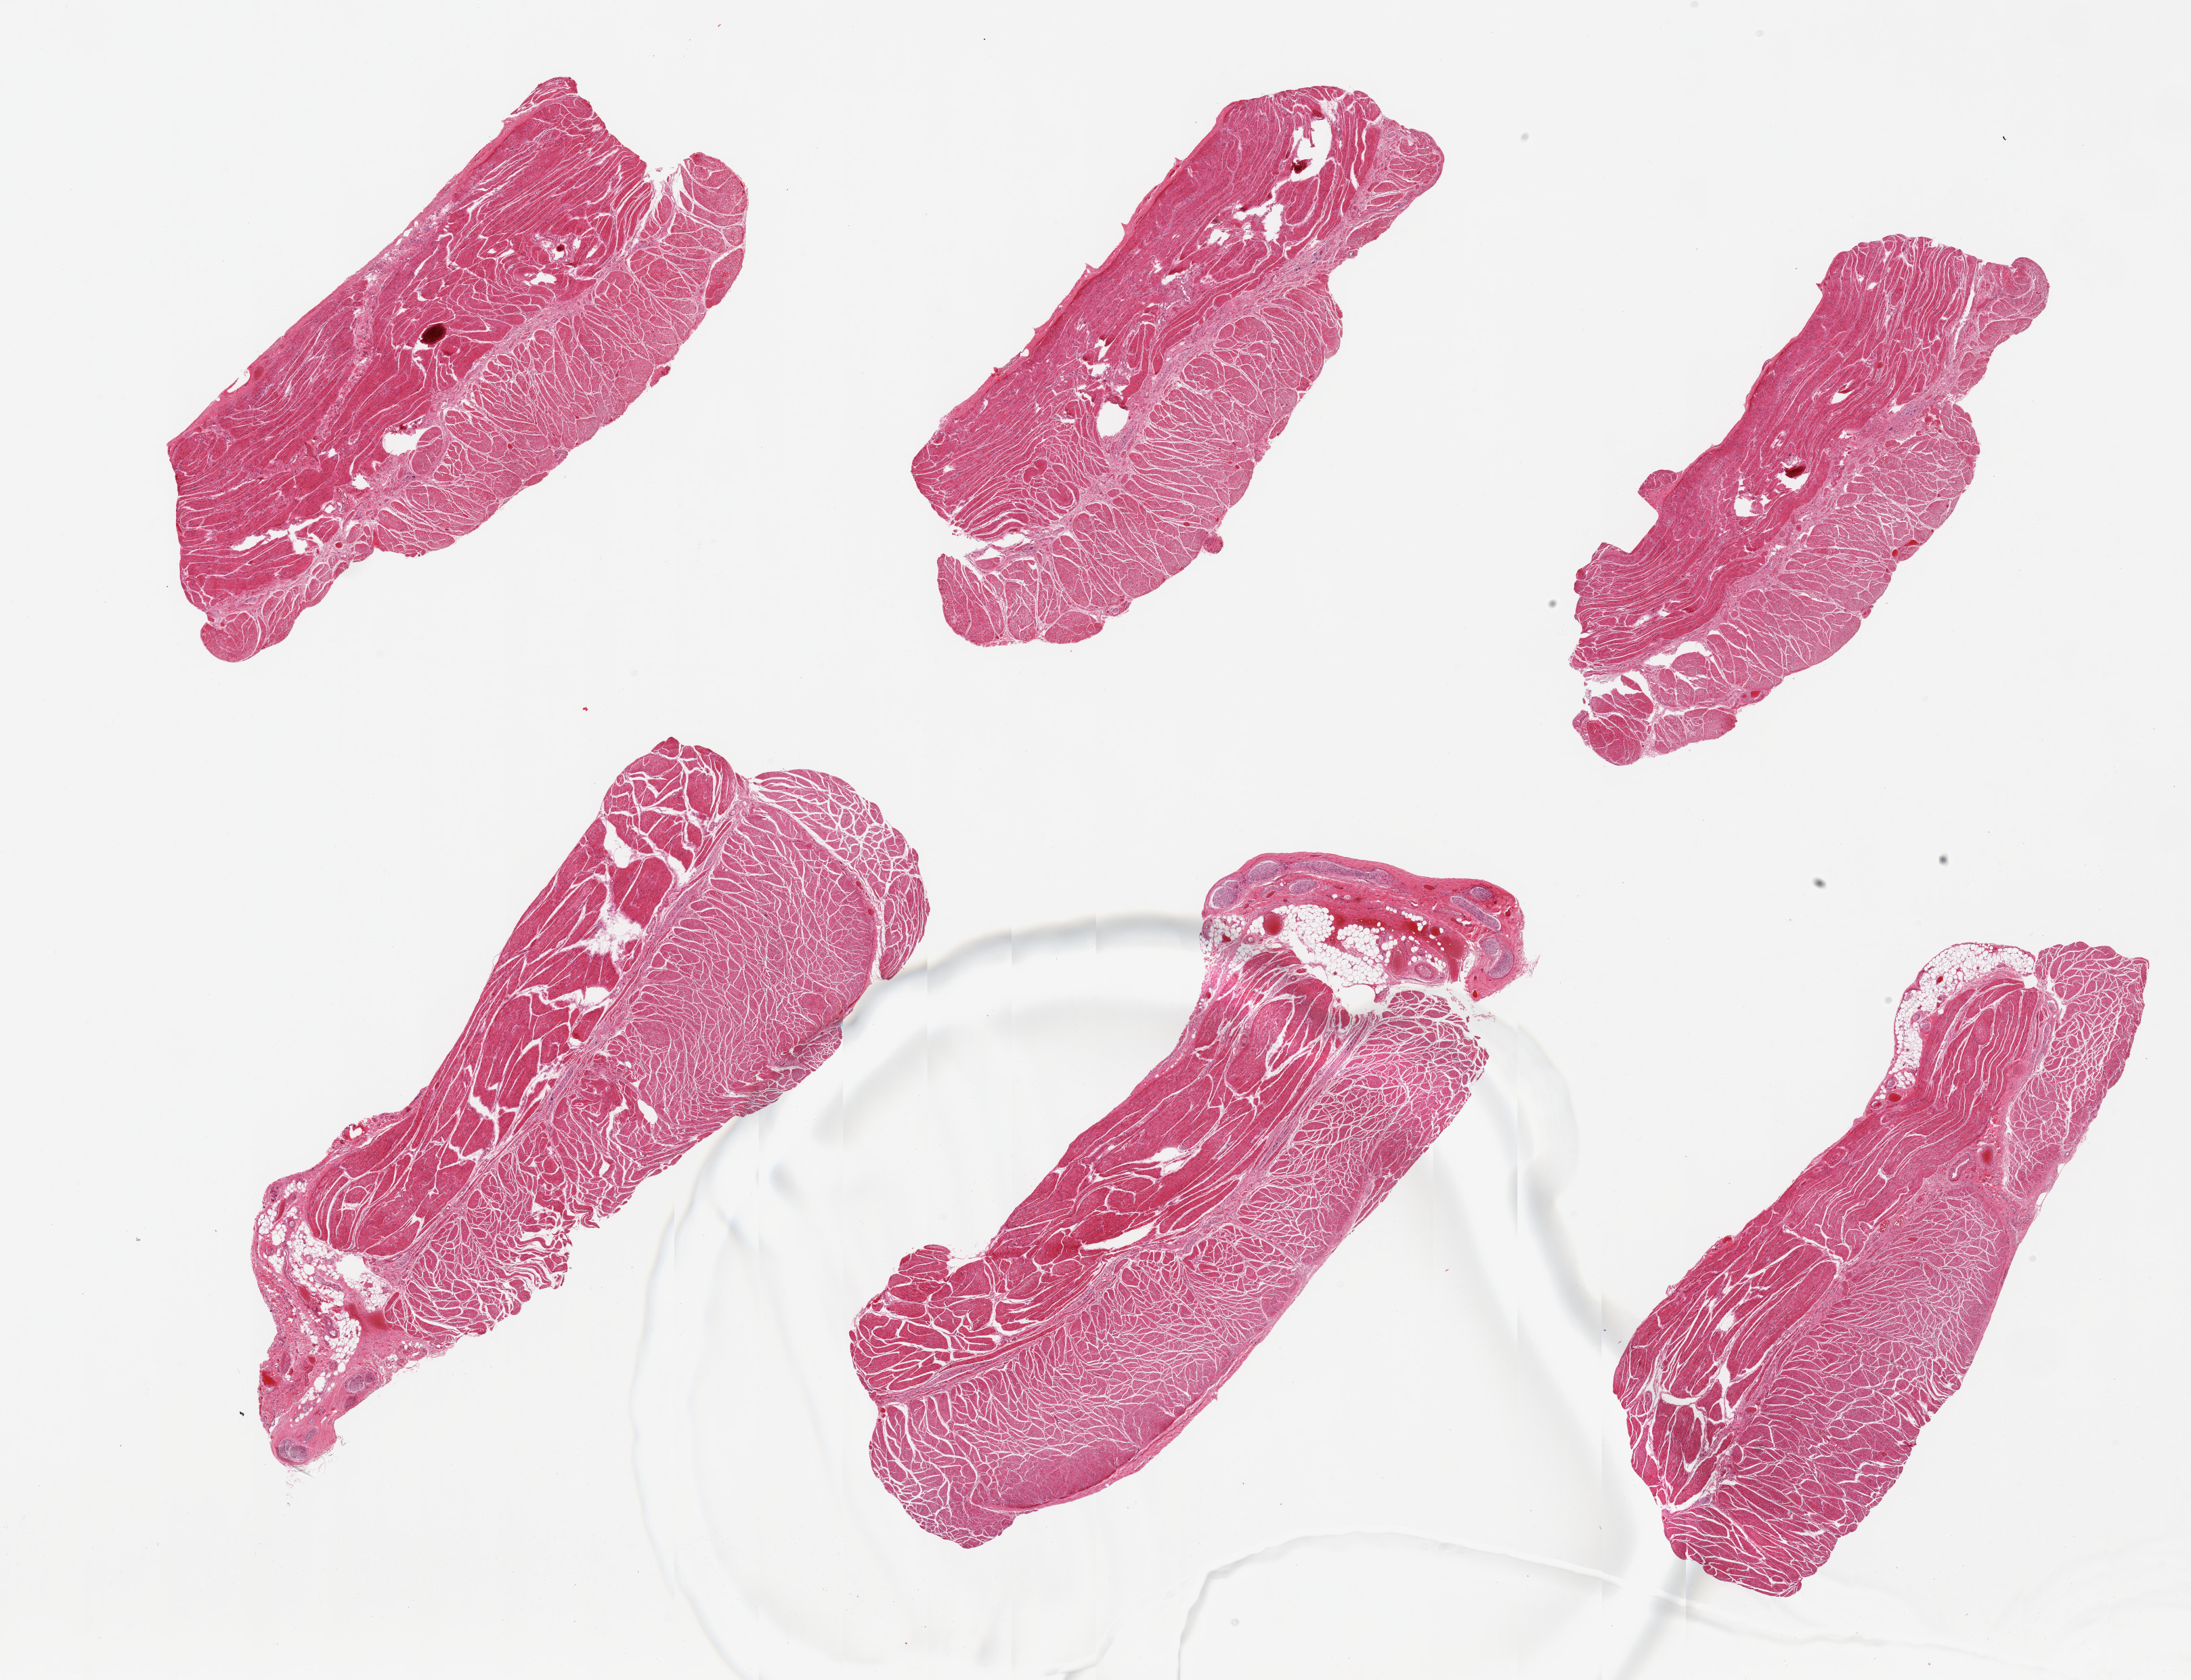
Digitized H&E-stained section, shown as a low-resolution overview of the whole scanned area (about 25.6 x 19.6 mm, slide scanned at 20x); PAXgene-fixed paraffin-embedded (PFPE) section; sampled site (target tissue): esophageal muscle; tissue donor sample. Donor: male.
Review note (as recorded): 6 pieces; predominantly well trimmed, few with attachments of fat and nerve.